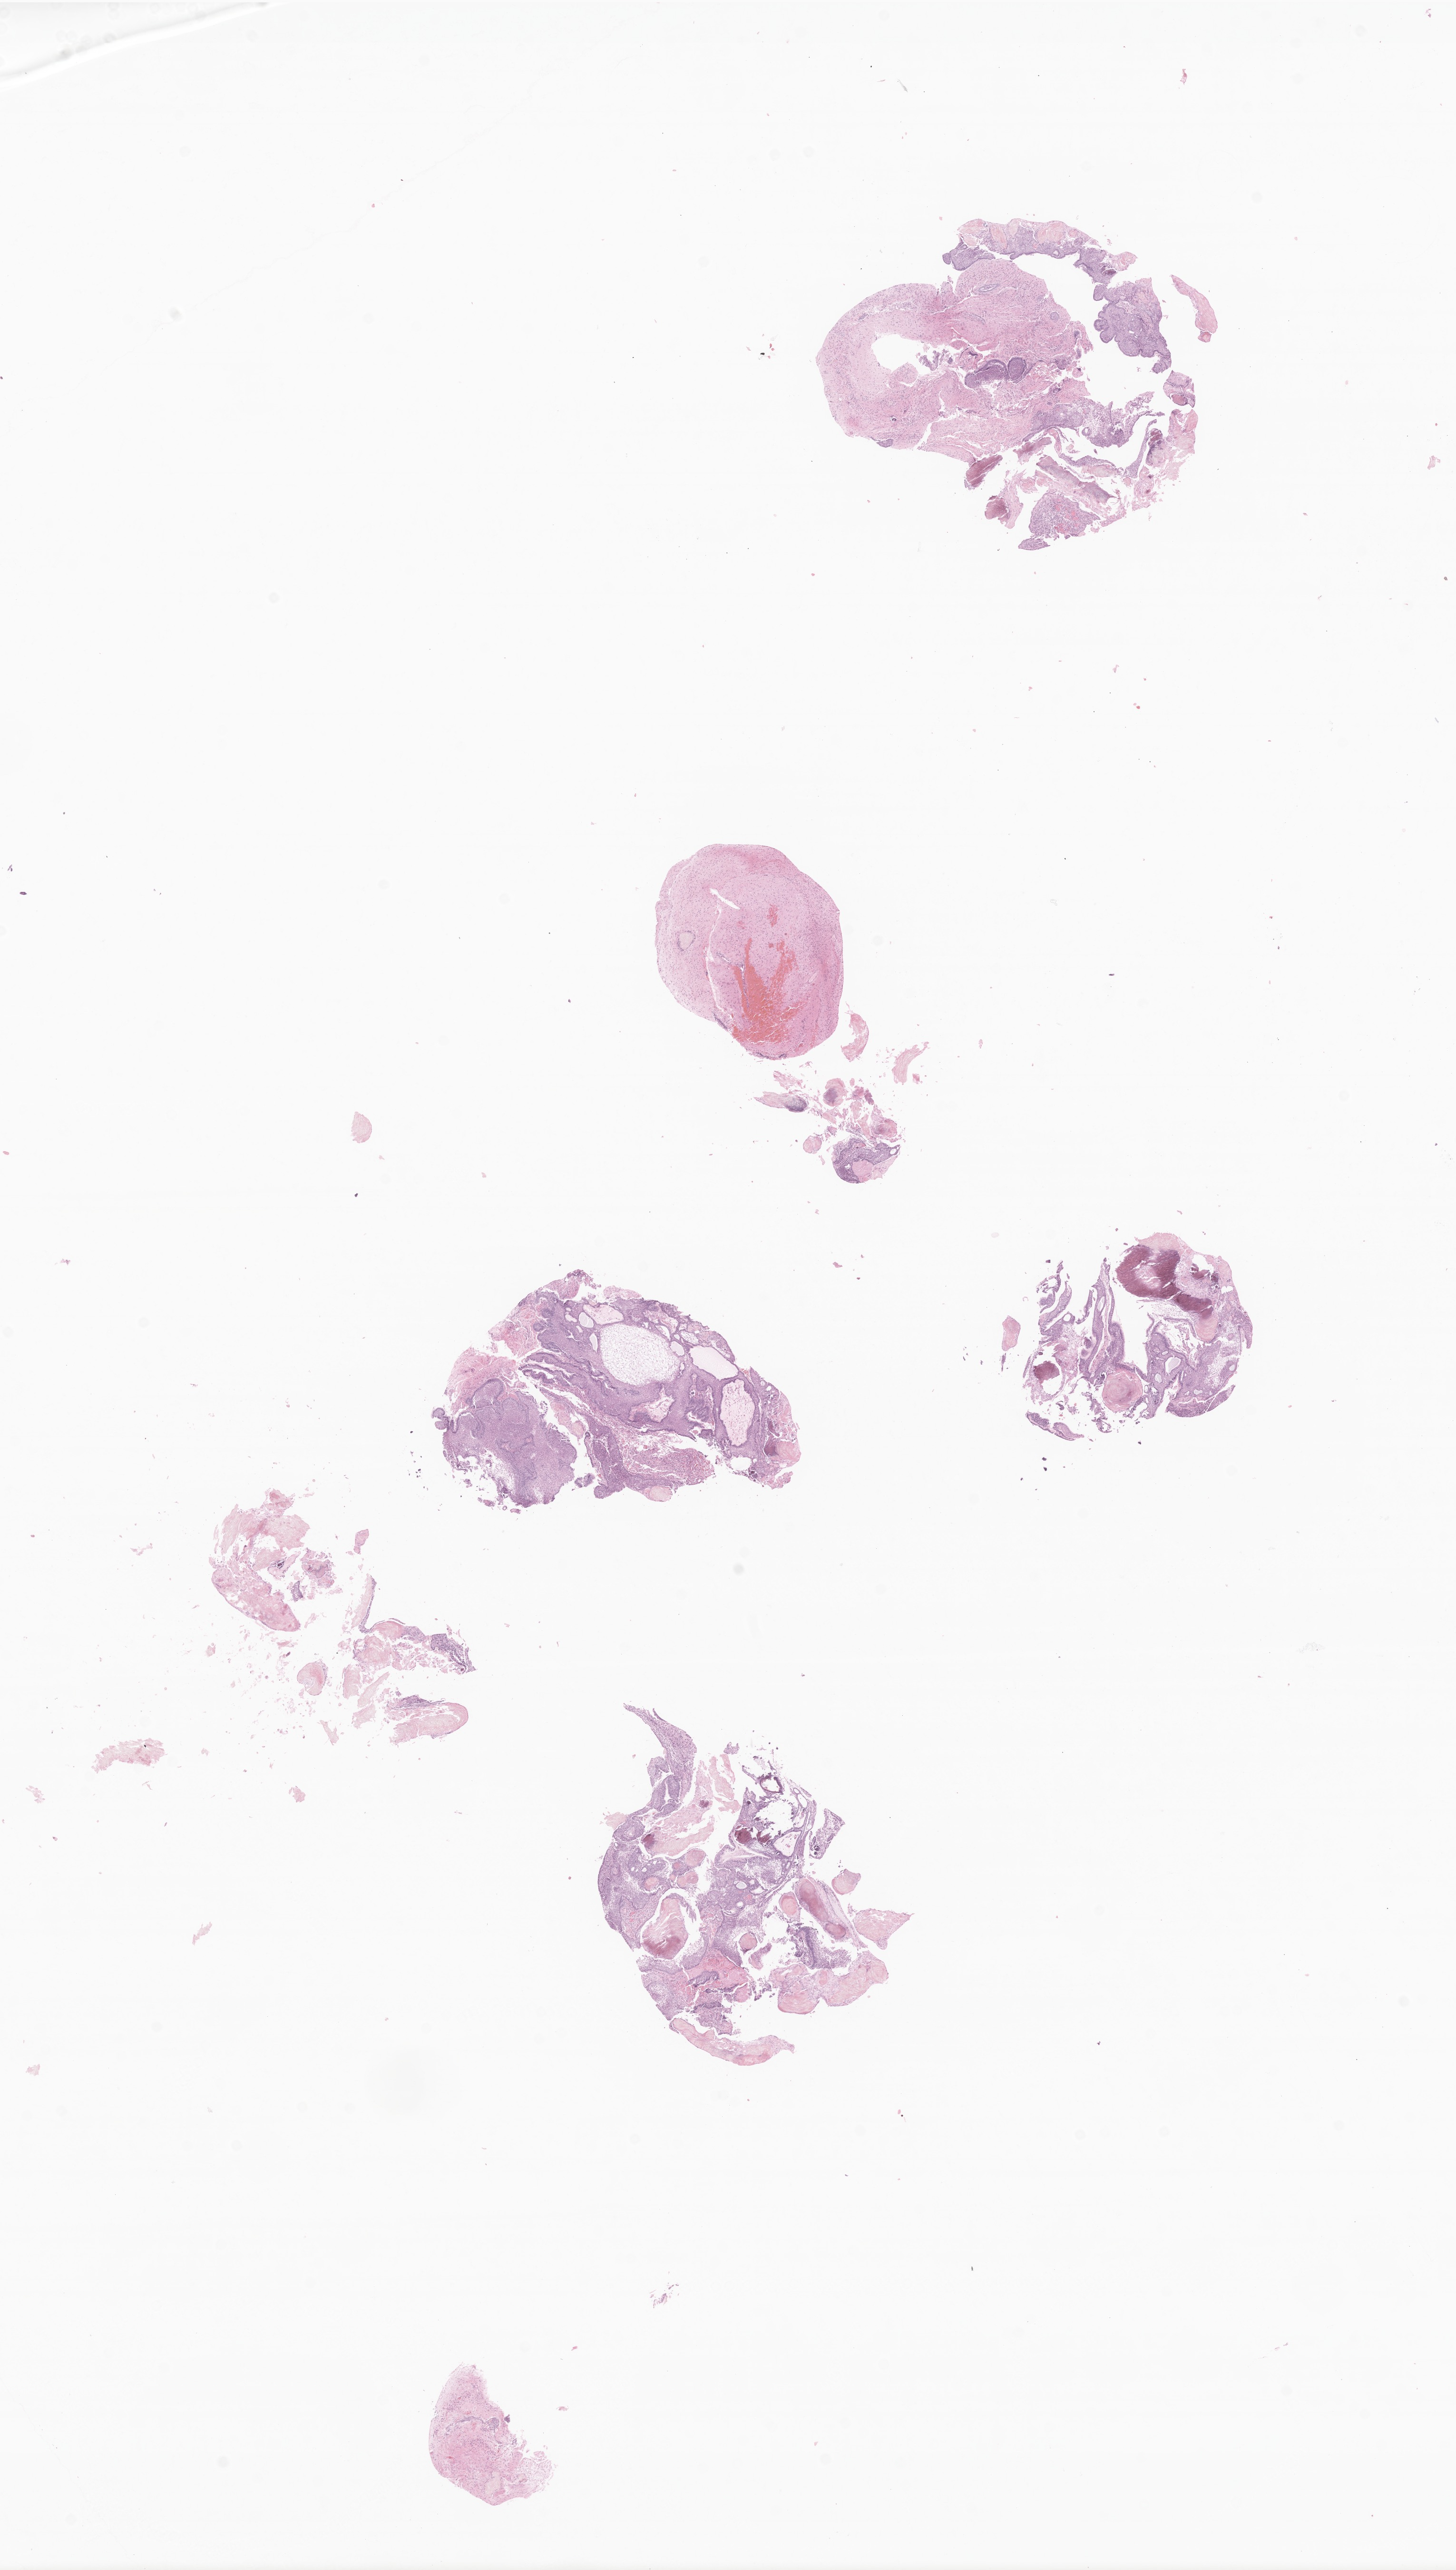
Digitized H&E-stained section of tumor tissue from the brain — shown as a low-resolution overview of the whole scanned area (about 12.9 x 22.8 mm), FFPE section. Patient: male, age 59 months.
* recorded diagnosis: Craniopharyngioma, adamantinomatous